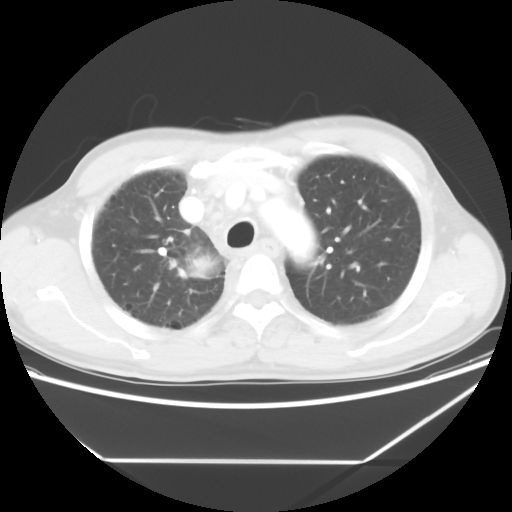
Chest CT, one axial slice. Slice 46 of 60 in the series (ordered by position). Lung window (W 1500 / L -600 HU). 512 × 512 image matrix, field of view 367 × 367 mm. Patient: male, 58 years. Case-level facts recorded for this patient, not image findings: clinical TNM (as recorded): T2 N2 M0.
Structures marked on this image (rectangle marked by the reading radiologist):
- lung tumour (recorded histology: squamous cell carcinoma): box from (x=186, y=254) to (x=216, y=280) px